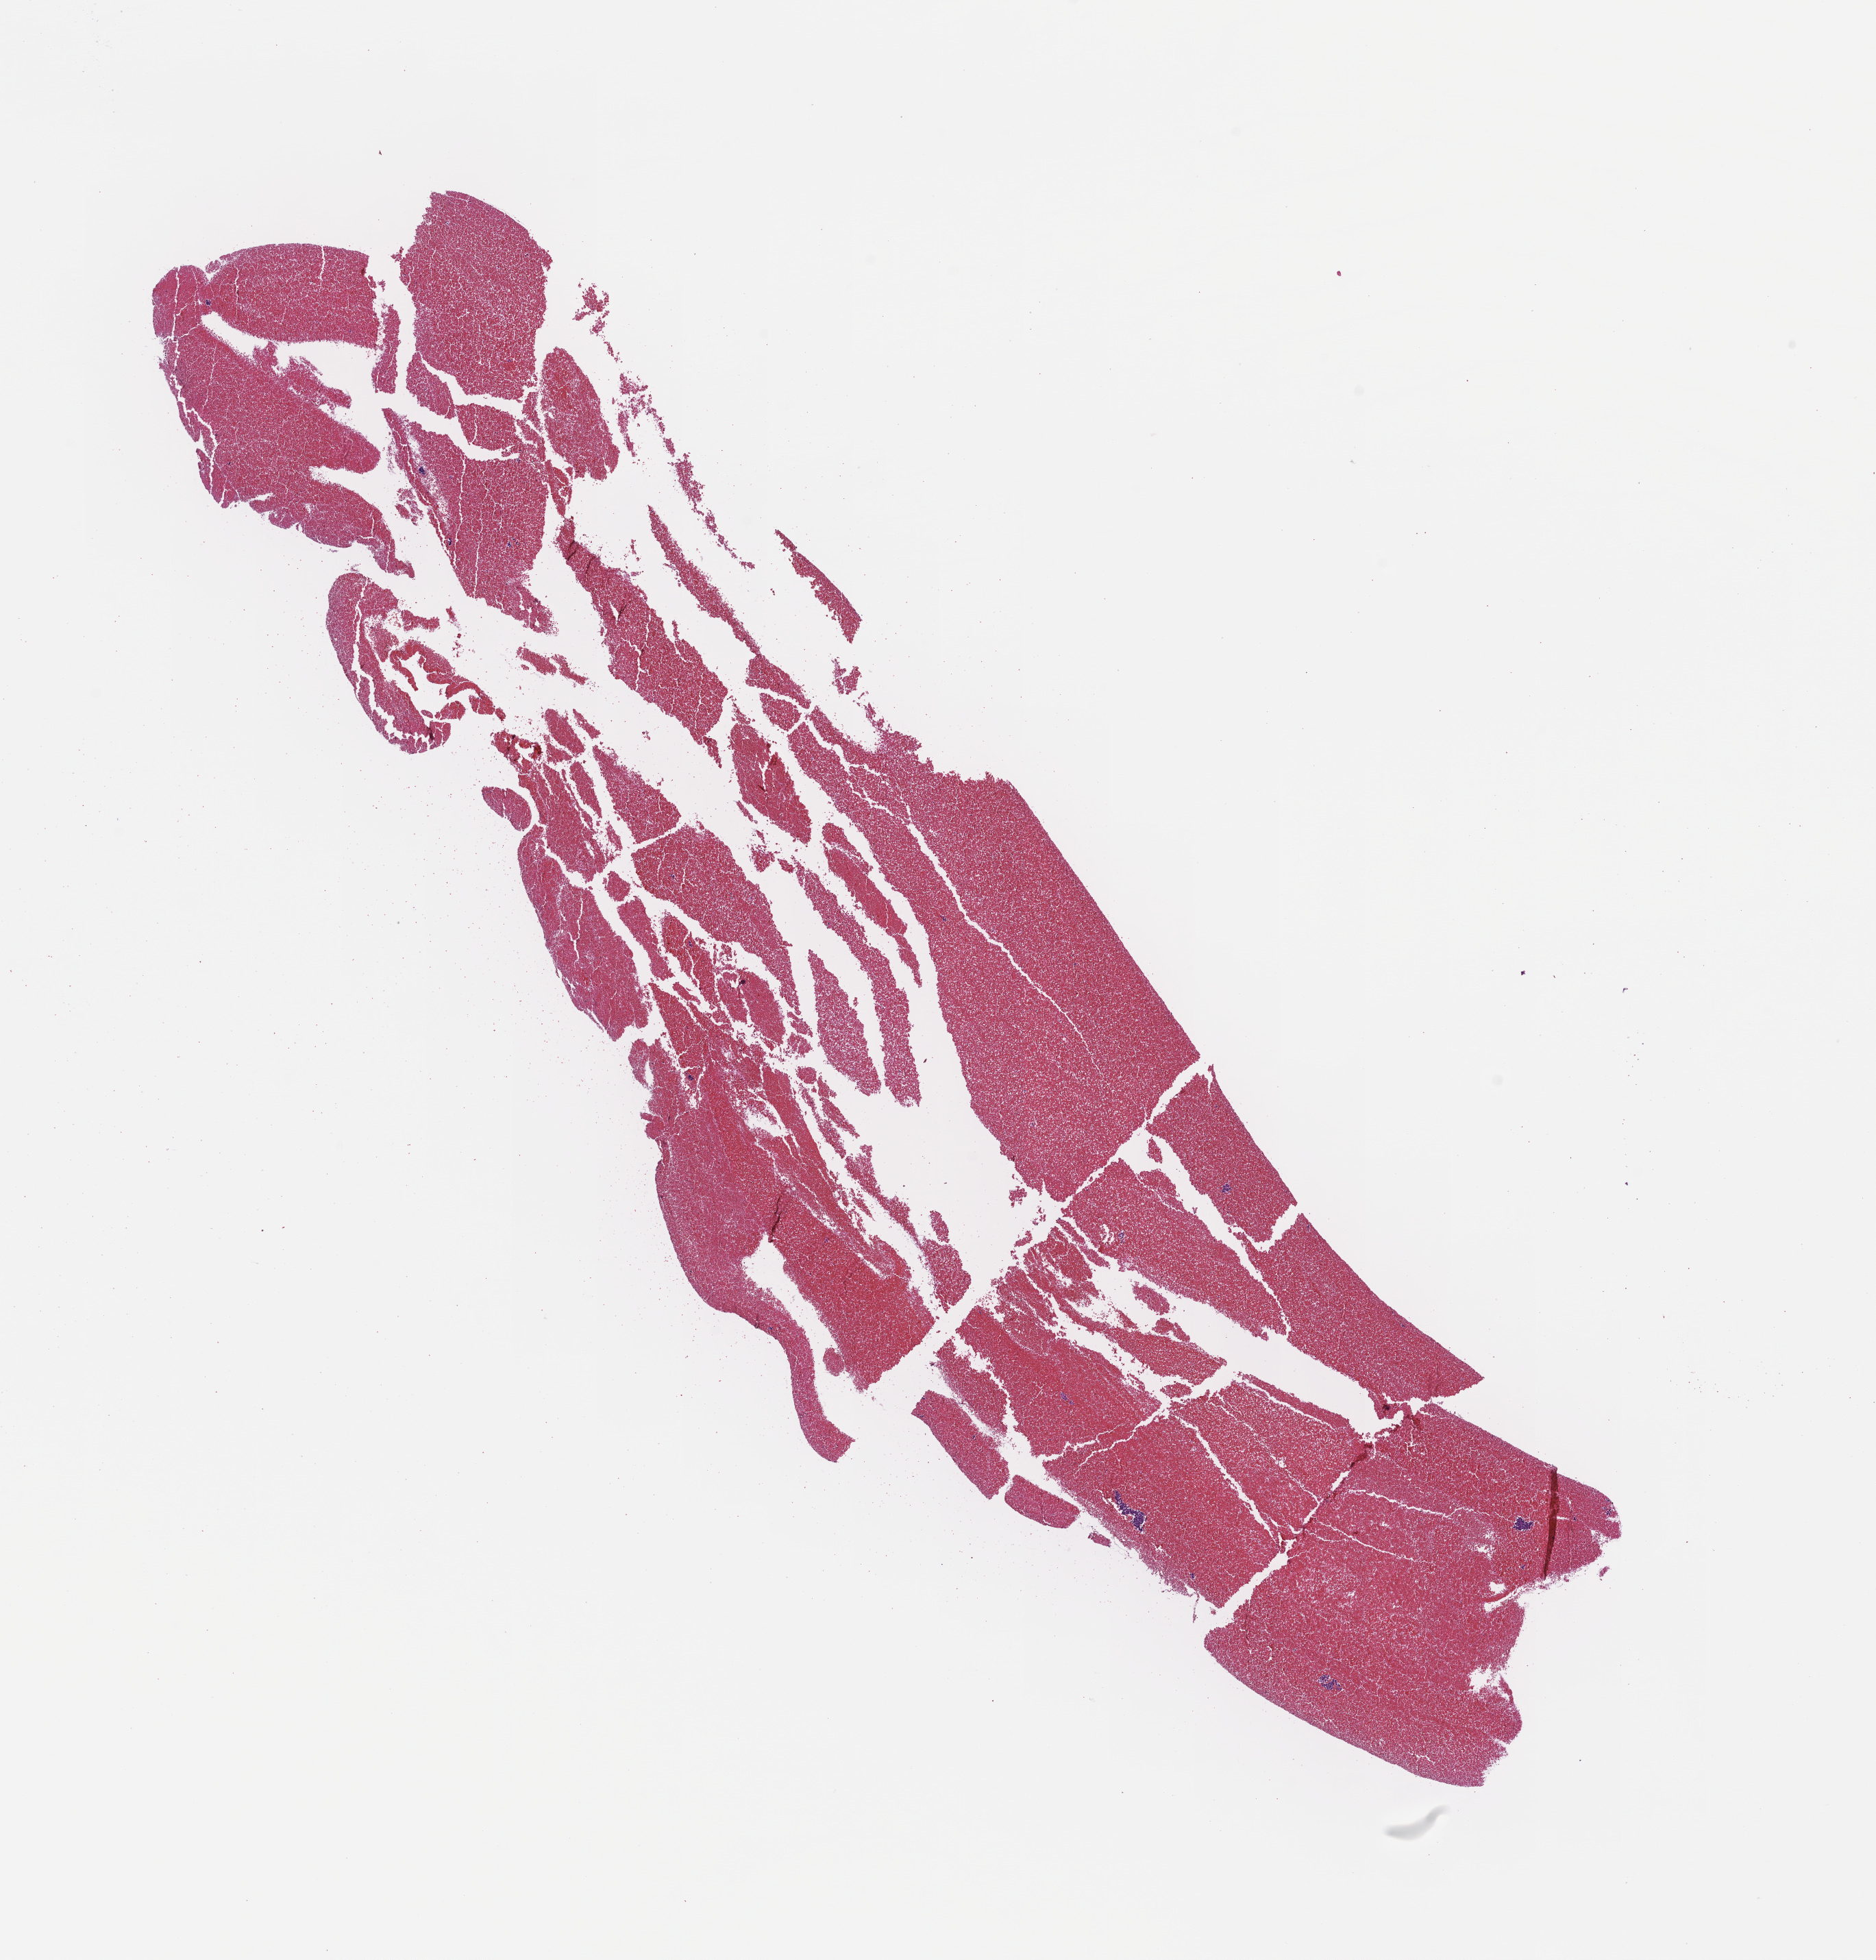
Digitized H&E-stained section — shown as a low-resolution overview of the whole scanned area (about 11.1 x 11.5 mm). Formalin-fixed paraffin-embedded section. Specimen time point: archival tissue. Male patient.
This section: metastasis (sampled organ not recorded). Patient diagnosis (primary): Prostate Carcinoma.